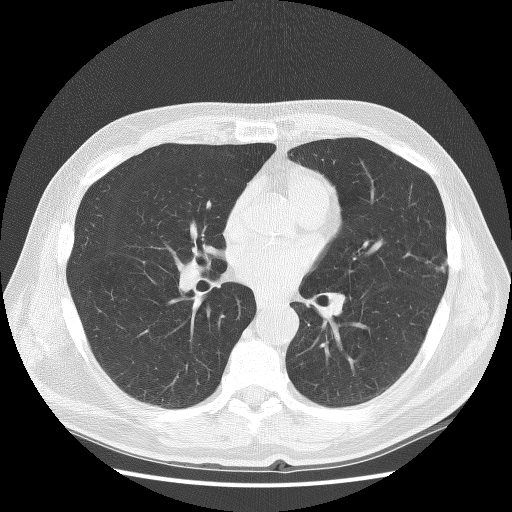
Low-dose screening chest CT, axial slice. Baseline screening round. Lung window (W 1500 / L -600 HU). 2.5 mm slice thickness. 120 kVp. Slice 124 of 272 in the series. 512 × 512 image matrix, field of view 360 × 360 mm. Male, age 67 years at enrolment.
Lesion marked by an expert reader, bounding box [x1, y1, x2, y2] px = [404, 244, 463, 294]. Screening reader's record for this exam: no non-calcified nodule ≥4 mm recorded. Official screen result: negative screen, minor abnormalities not suspicious for lung cancer. Later outcome: lung cancer diagnosed 772 days after this screen (after the third annual screen) — squamous cell carcinoma, NOS, left upper lobe, moderately differentiated (G2), stage IB (AJCC 6th edition), 25 mm at pathology.